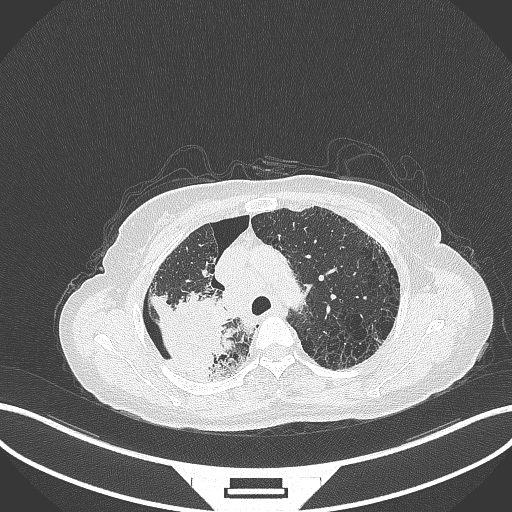
Chest CT, one axial slice; position 262 of 408 along the scan axis; 120 kVp; lung window (W 1500 / L -600 HU); 512 × 512 image matrix, field of view 400 × 400 mm. Patient: female, 64 years. From the clinical record (not read from this slice): clinical TNM (as recorded): T3 N3 M0.
Outlined on this slice (rectangle marked by the reading radiologist):
- lung tumour (recorded histology: squamous cell carcinoma): bounding box [x1, y1, x2, y2] px = [150, 286, 226, 381]